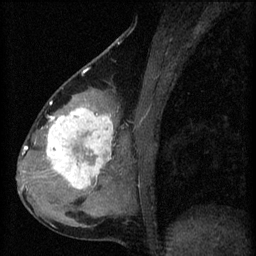
Breast MRI (dynamic contrast-enhanced), one sagittal slice. Position 27 of 60 along the scan axis. 3 images stored at this slice position (order not interpretable as contrast timing). 1.5 T. TE 4.2 ms, TR 8.2 ms. 2 mm slice thickness. 256 × 256 image matrix. Patient: female, 37 years.
Structures marked on this image (semi-automatically segmented with operator editing):
- analysis volume of interest (the breast-tissue region the enhancement analysis was run in; not a lesion): bounding box <44,100,119,197> (left, top, right, bottom; pixels)
- tumour enhancement mask (voxels above the 70 % enhancement threshold inside the analysis volume of interest): <47,108,114,189>